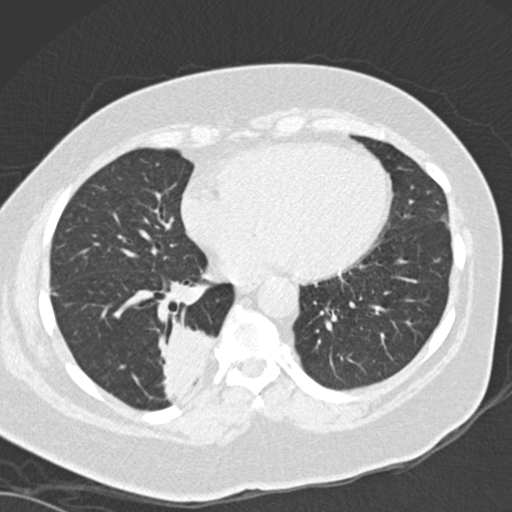
Low-dose screening chest CT, one axial slice. Slice 62 of 162 in the series (ordered by position). Lung window (W 1500 / L -600 HU). 512 × 512 image matrix.
Outlined on this slice (manually delineated by an expert):
- lesion 1 (tumor, lower lobe of right lung): box from (x=158, y=317) to (x=216, y=405) px